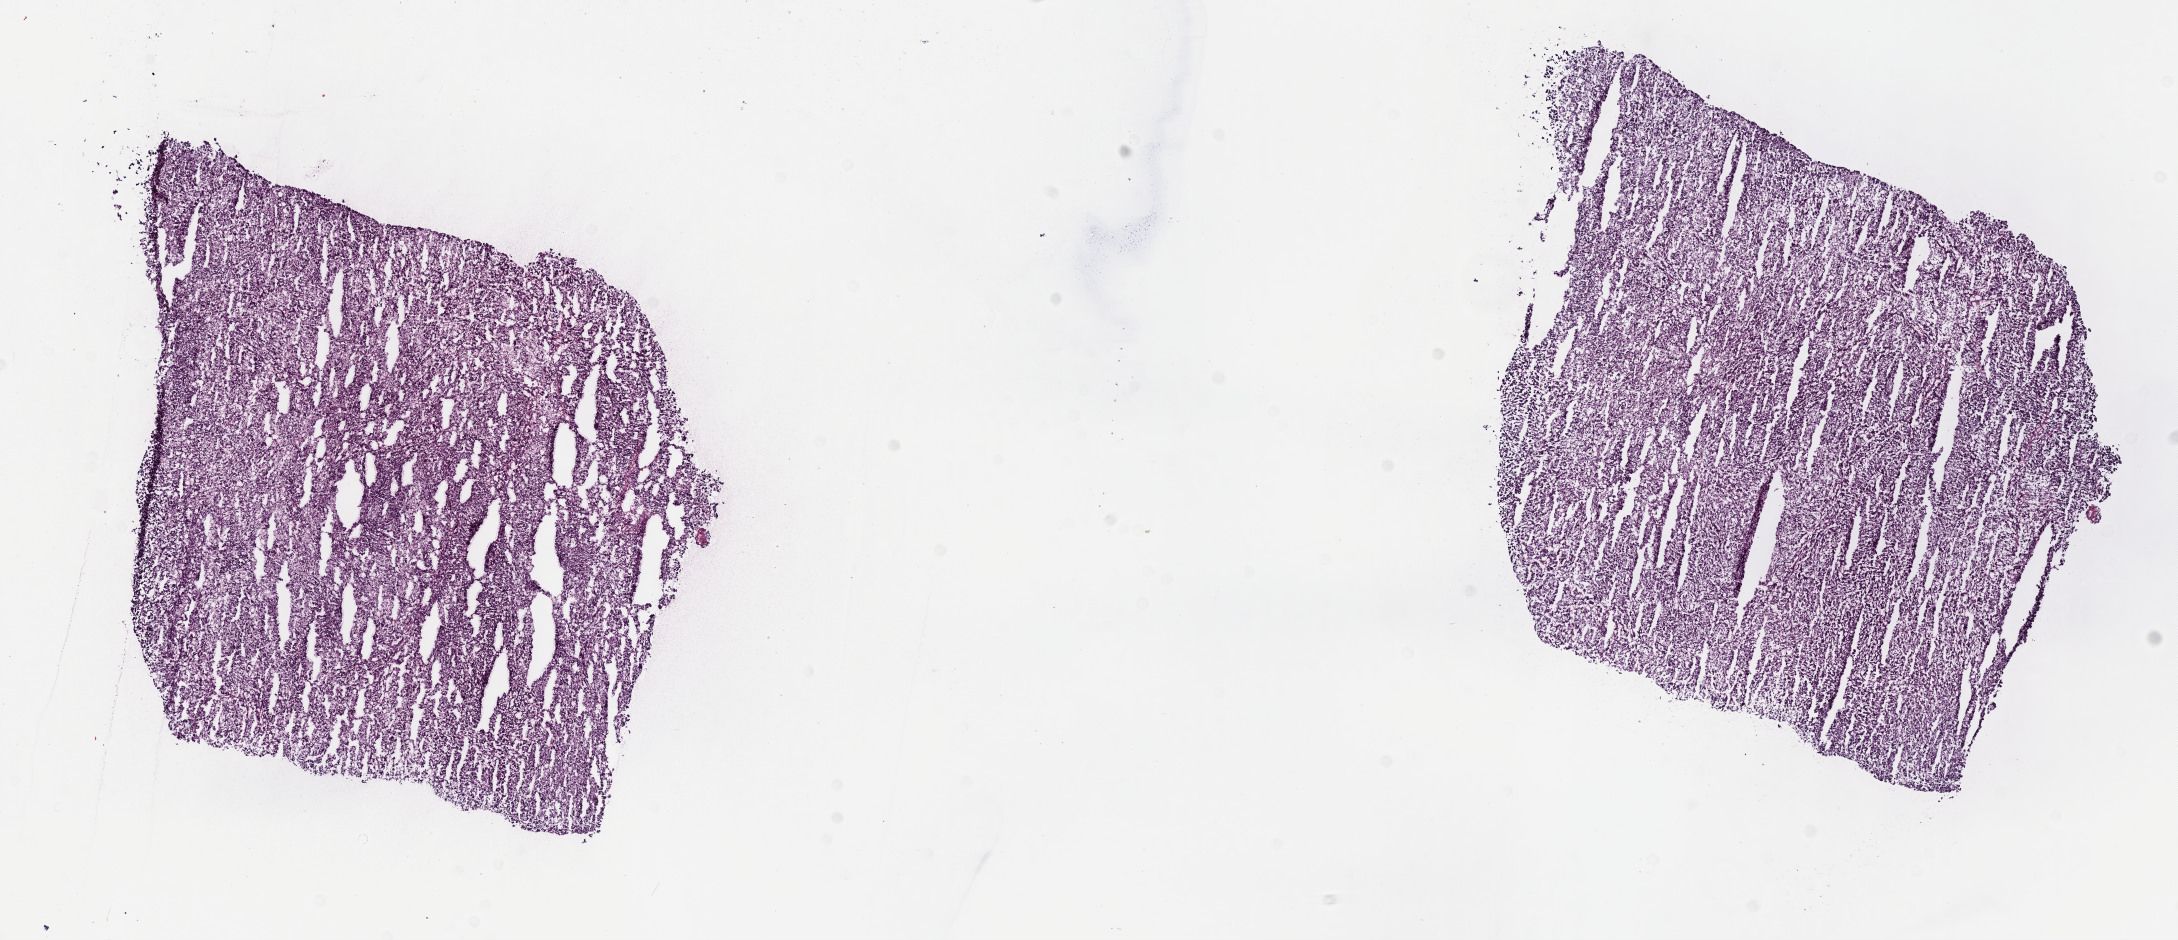
Whole-slide histology image, H&E, shown as a low-resolution overview of the whole scanned area (about 17.6 x 7.6 mm, slide scanned at 40x). Frozen section from the top of the tissue portion. Sample: primary tumour, liver. Male patient; age at initial diagnosis 50 years. Histologic grade: G3 (poorly differentiated). Slide review estimates, as recorded: tumour cells 100%, tumour nuclei 94%, normal cells 0%, stromal cells 0%, necrosis 0%. Inflammatory infiltration, as recorded: lymphocyte infiltration 0%, monocyte infiltration 0%, neutrophil infiltration 0%.
Pathologic diagnosis: Hepatocellular carcinoma, NOS. AJCC pathologic stage: II (6th edition).